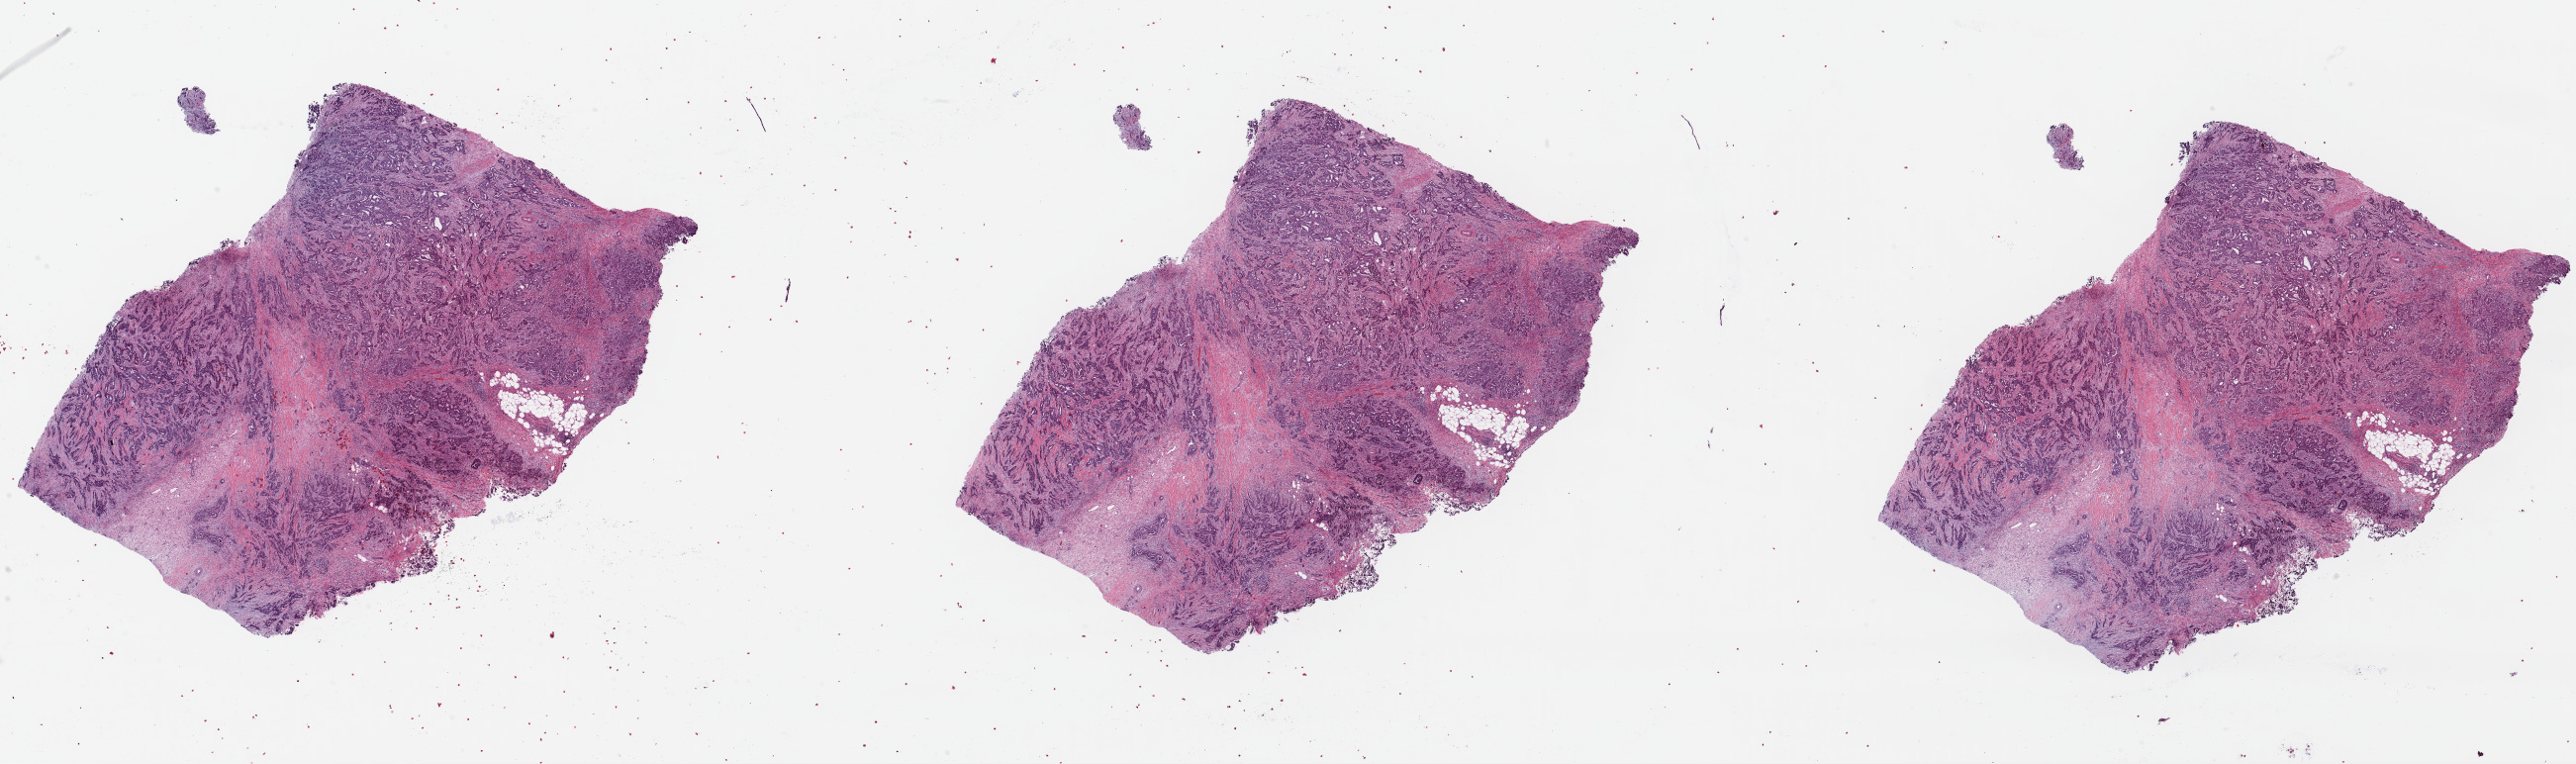
Digitized H&E tissue section (whole slide) — shown as a low-resolution overview of the whole scanned area (about 40.9 x 12.1 mm, from a 40x scan). Formalin-fixed paraffin-embedded (FFPE) diagnostic section. Breast, primary tumour sample. Patient: female, age at initial diagnosis 53 years.
AJCC pathologic stage: IIIA (7th edition). Lymph nodes positive (case pathology): 8 of 10 examined. Laterality: right. Pathologic diagnosis: Infiltrating duct carcinoma, NOS.